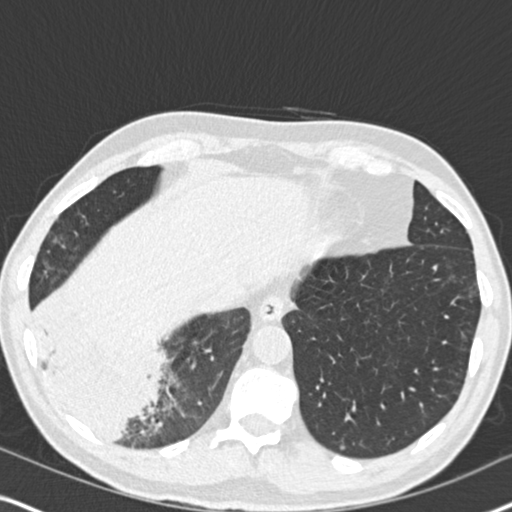
Low-dose screening chest CT, one axial slice. Slice 54 of 182 in the series (ordered by position). Reconstruction kernel B30f. Lung window (W 1500 / L -600 HU). 2 mm slice thickness. 512 × 512 image matrix.
Structures marked on this image (outlined manually by an expert reader):
- lesion 1 (tumor, lower lobe of right lung): bounding box <41,325,161,436> (left, top, right, bottom; pixels)